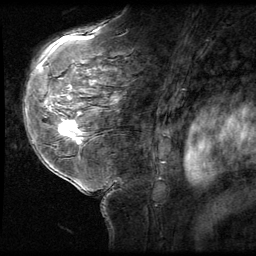
Breast MRI (dynamic contrast-enhanced), one sagittal slice. 3 images stored at this slice position (order not interpretable as contrast timing). 1.5 T. TE 4.2 ms, TR 9 ms. 2.5 mm slice thickness. 256 × 256 image matrix. Female patient, age 58 years. From the clinical record (not read from this slice): setting: breast cancer imaged before/during neoadjuvant chemotherapy; receptor status: HR-positive, HER2-negative.
Structures marked on this image (semi-automatic segmentation, software-assisted and operator-edited):
- analysis volume of interest (the breast-tissue region the enhancement analysis was run in; not a lesion): bounding box (x1, y1, x2, y2) in pixels: (51, 116, 93, 151)
- tumour enhancement mask (voxels above the 140 % enhancement threshold inside the analysis volume of interest): (60, 120, 84, 143)